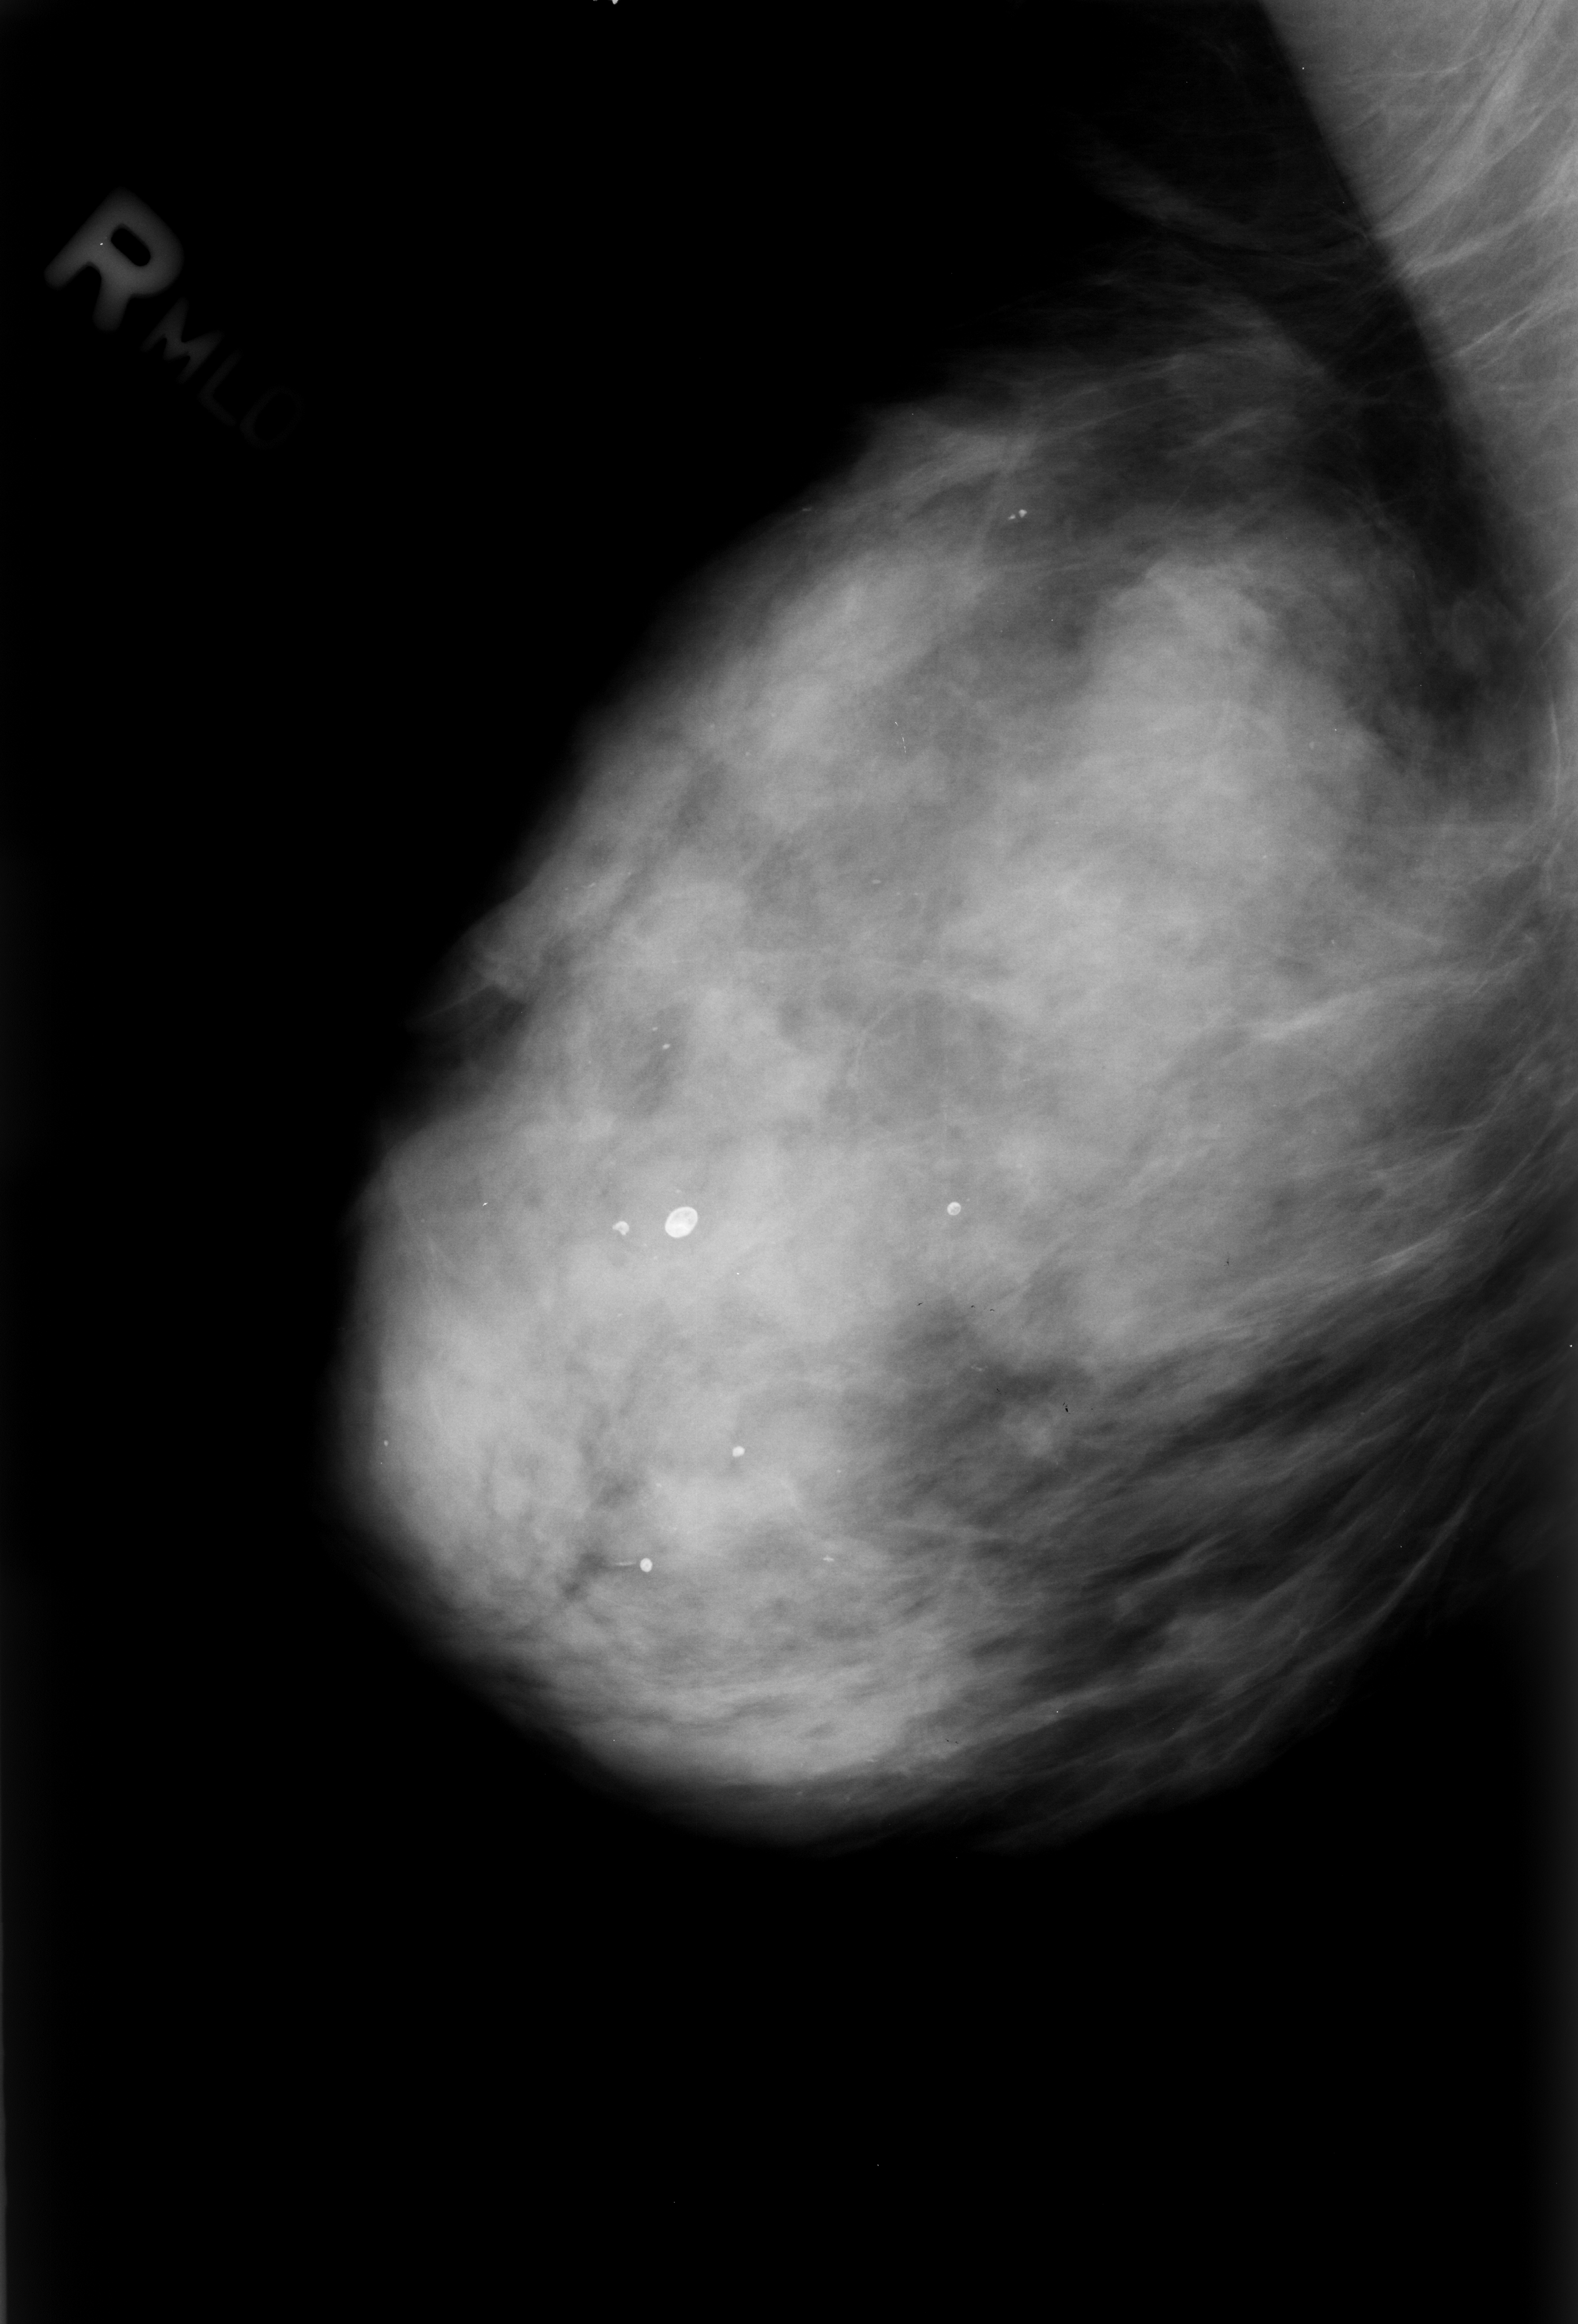
Mammogram (digitized film); right breast; mediolateral oblique (MLO) view; breast composition: extremely dense (BI-RADS density category 4 of 4).
- Abnormality record for this image: Finding 1 of 6: calcifications, morphology round and regular / lucent center / punctate, distribution diffusely scattered; BI-RADS assessment category 2; subtlety rating 5 on a 1 (subtle) to 5 (obvious) scale; benign without callback (not worked up further).
- Finding 2 of 6: calcifications, morphology round and regular / lucent center / punctate, distribution diffusely scattered; BI-RADS assessment category 2; subtlety rating 5 on a 1 (subtle) to 5 (obvious) scale; benign; no additional work-up was recommended (benign without callback).
- Finding 3 of 6: calcifications, morphology round and regular / lucent center / punctate, distribution diffusely scattered; BI-RADS assessment category 2; subtlety rating 5 on a 1 (subtle) to 5 (obvious) scale; benign without callback (not worked up further).
- Finding 4 of 6: calcifications, morphology round and regular / lucent center / punctate, distribution diffusely scattered; BI-RADS assessment category 2; subtlety rating 5 on a 1 (subtle) to 5 (obvious) scale; benign without callback (not worked up further).
- Finding 5 of 6: calcifications, morphology round and regular / lucent center / punctate, distribution diffusely scattered; BI-RADS assessment category 2; subtlety rating 5 on a 1 (subtle) to 5 (obvious) scale; benign without callback (not worked up further).
- Finding 6 of 6: calcifications, morphology round and regular / lucent center / punctate, distribution diffusely scattered; BI-RADS assessment category 2; subtlety rating 5 on a 1 (subtle) to 5 (obvious) scale; benign; no additional work-up was recommended (benign without callback).